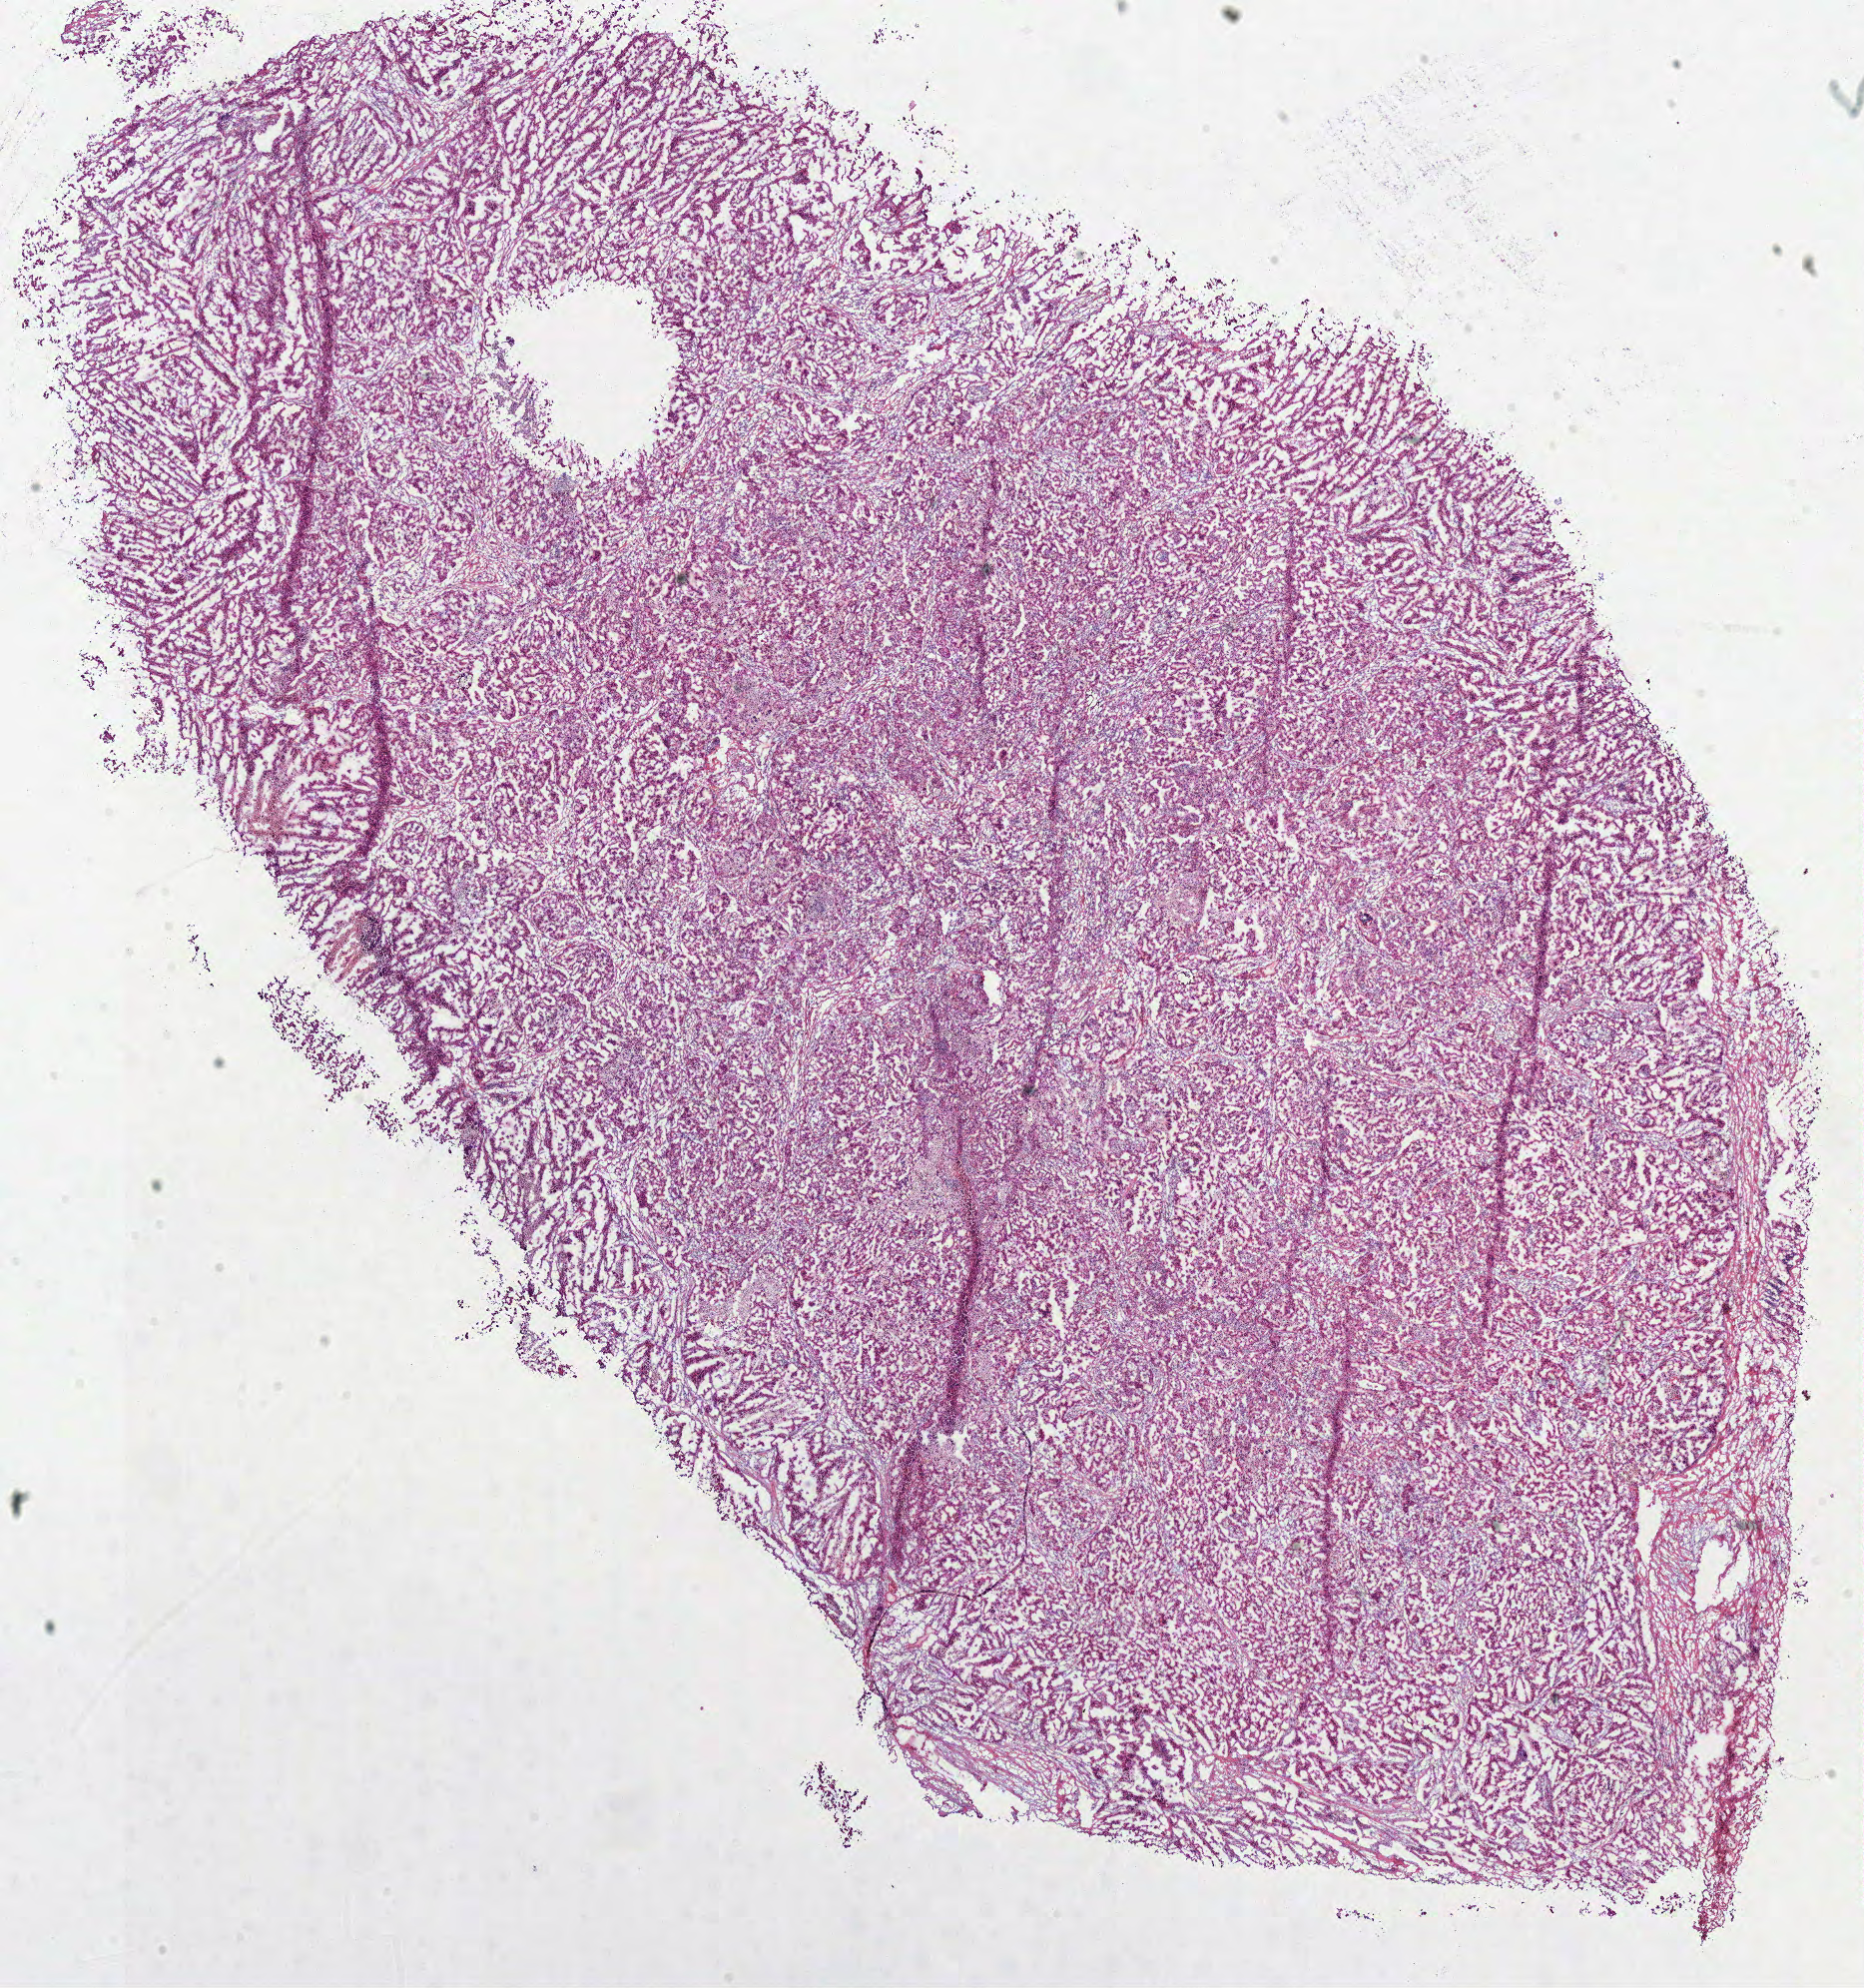
Whole-slide histology image, H&E — shown as a low-resolution overview of the whole scanned area (about 14.7 x 15.7 mm, slide scanned at 40x), frozen section, lung, primary tumour sample. Patient: female, age at initial diagnosis 48 years. Slide review estimates, as recorded: tumour cells 79%, tumour nuclei 75%, normal cells 8%, stromal cells 10%, necrosis 3%.
- diagnosis: Papillary adenocarcinoma, NOS (upper lobe, lung)
- AJCC pathologic stage: IB (6th edition)
- TNM: T2 N0 M0